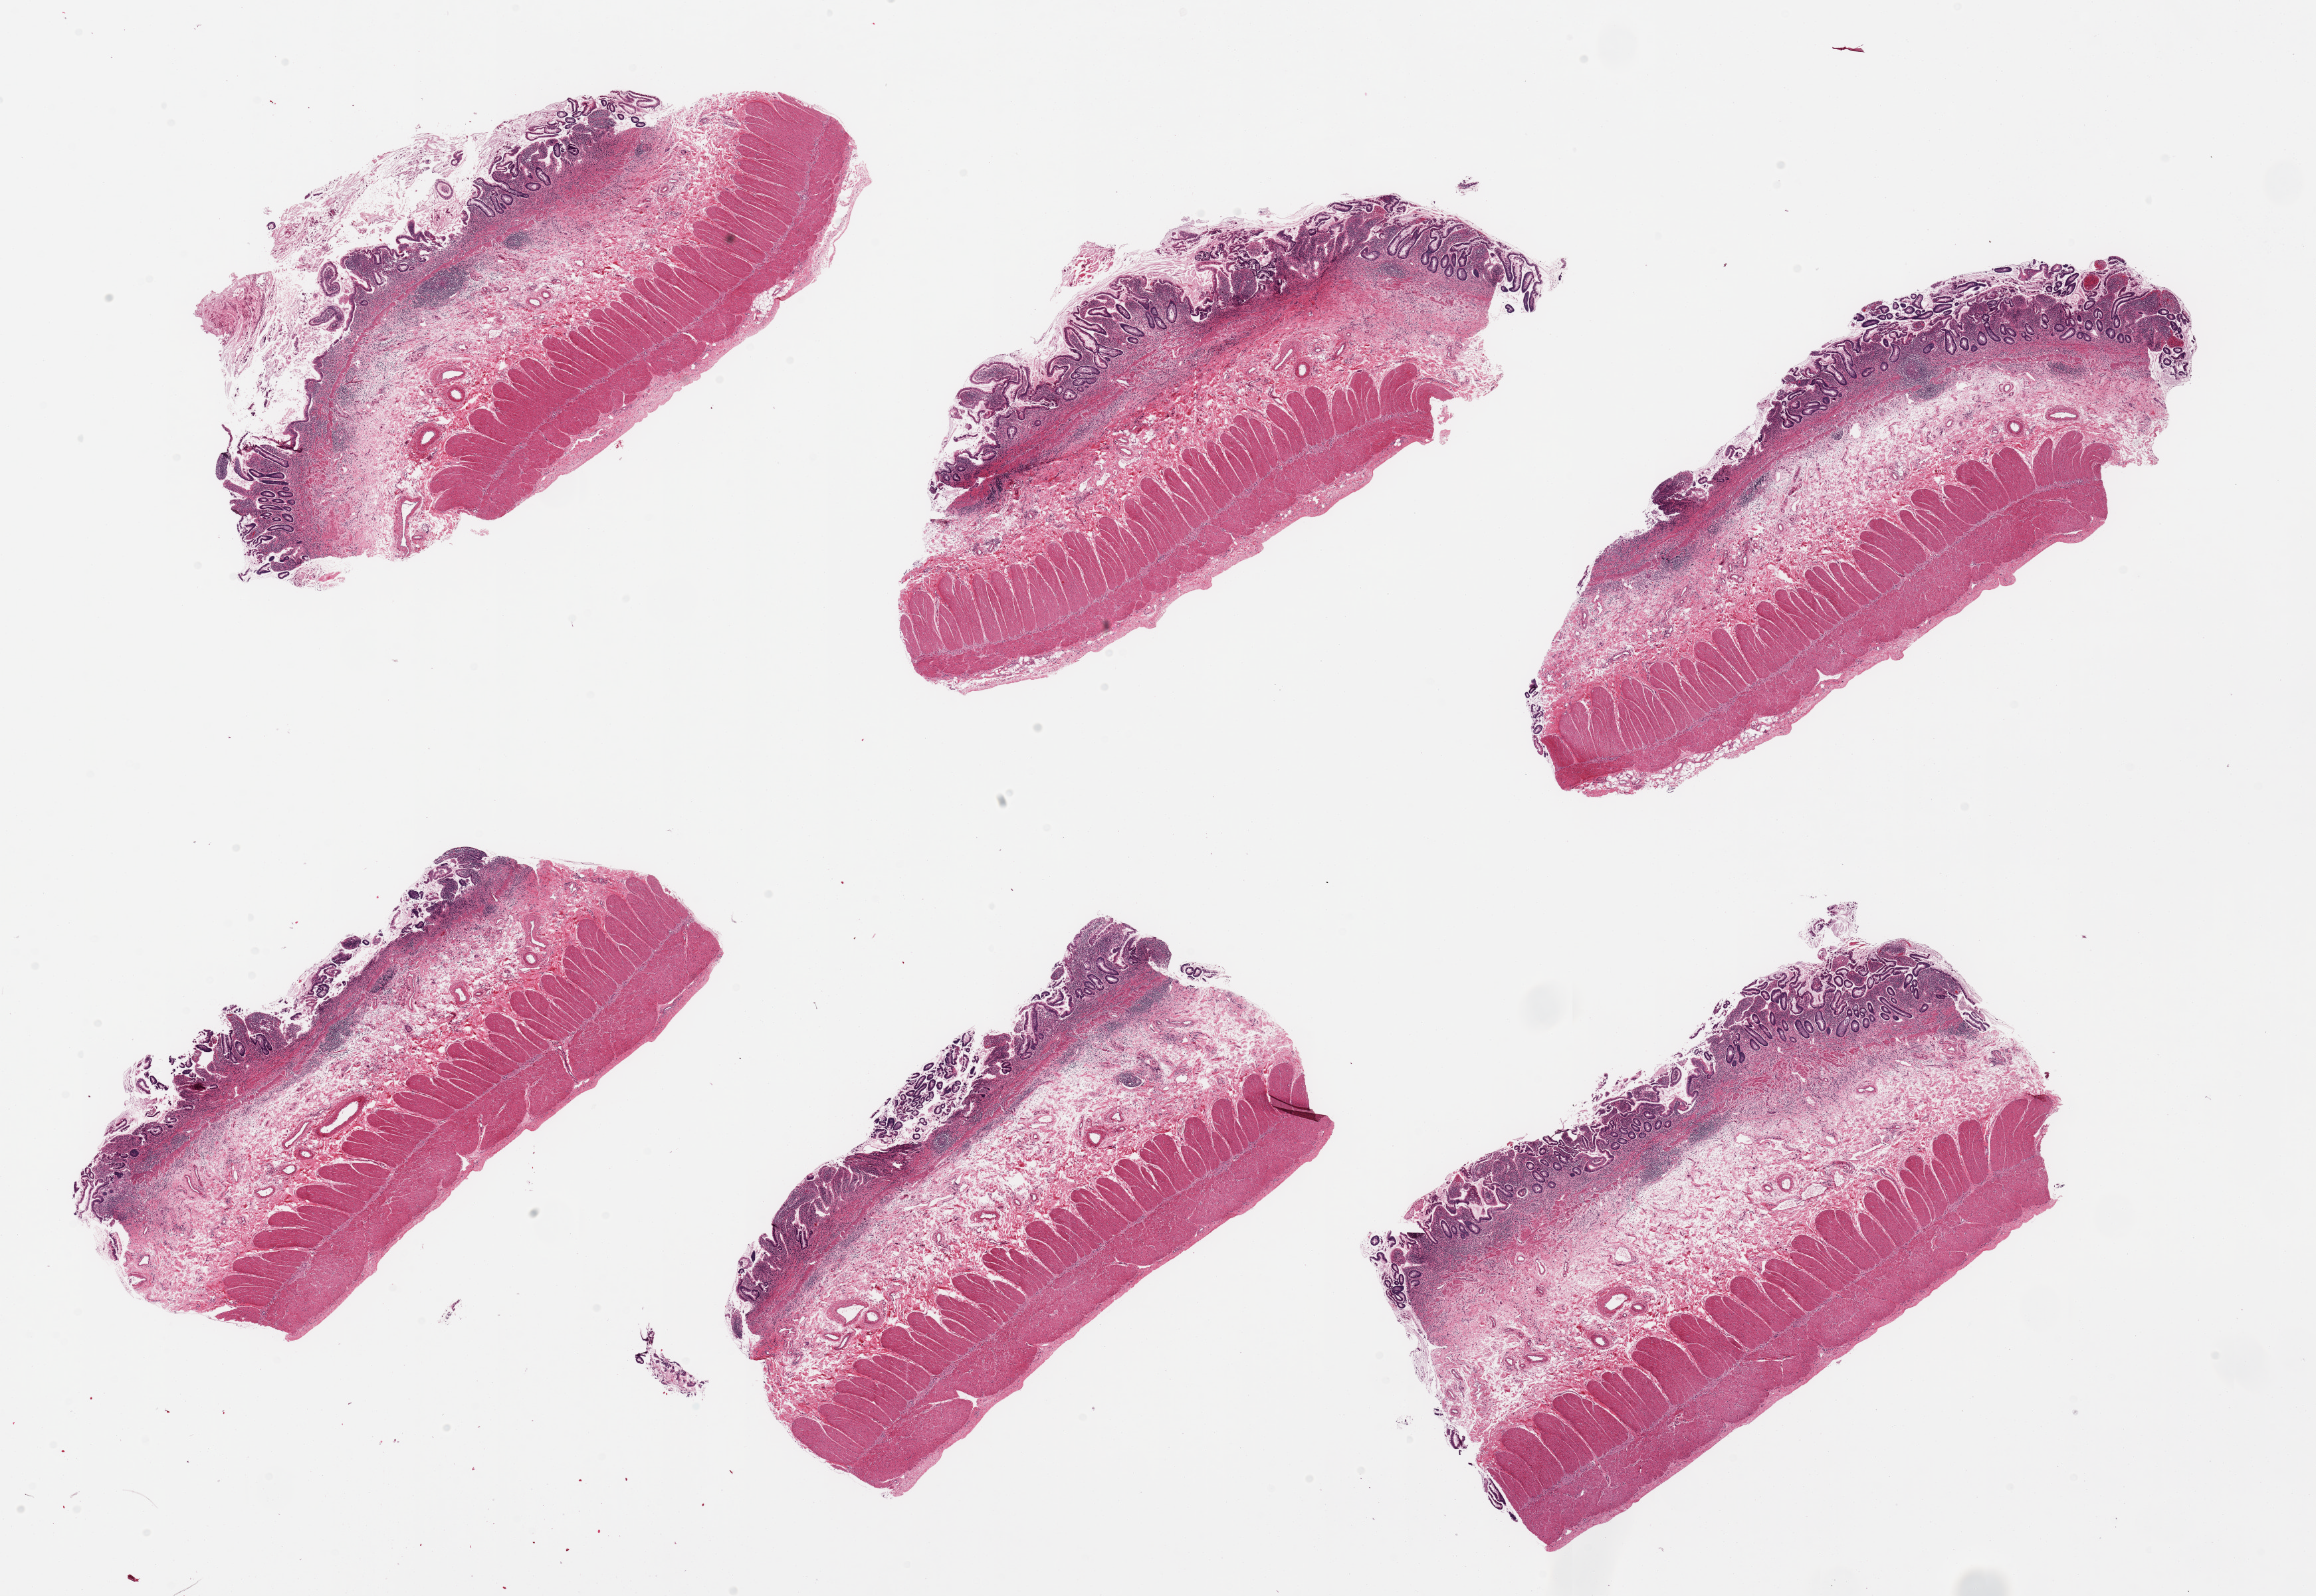
Digitized haematoxylin and eosin-stained section — shown as a low-resolution overview of the whole scanned area (about 27.6 x 19.0 mm), PAXgene-fixed, paraffin-embedded tissue, target tissue: sigmoid colon, donor tissue sample. Donor: female.
- pathologist's review note for this sample: 6 pieces; full thickness (mucosa not target), chronic colitis